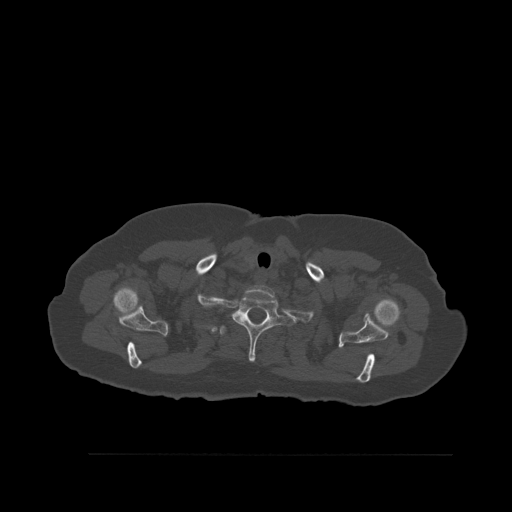
CT including the spine, one axial slice. Bone window (W 1800 / L 400 HU). 512 × 512 image matrix. Patient: female, 73 years. From the clinical record (not read from this slice): primary cancer: breast; vertebrae with lytic lesions (as recorded): L2.
Structures marked on this image (semi-automatic segmentation, software-assisted and operator-edited):
- T1 vertebra: bounding box [x1, y1, x2, y2] px = [232, 294, 295, 362]
- T2 vertebra: [222, 333, 225, 336]